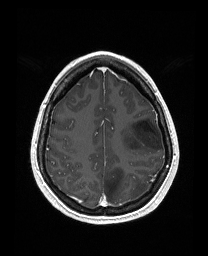
Brain MRI from a brain-tumour surgery series, one axial slice; position 121 of 176 along the scan axis; T1-weighted post-contrast; 208 × 256 image matrix, field of view 203 × 250 mm. From the clinical record (not read from this slice): histopathology: Astrocytoma; WHO grade: 3; IDH mutation: yes; tumour location: Left Frontal.
Annotated regions visible in this slice (expert manual segmentation):
- tumour: bounding box [x1, y1, x2, y2] px = [121, 116, 163, 152]